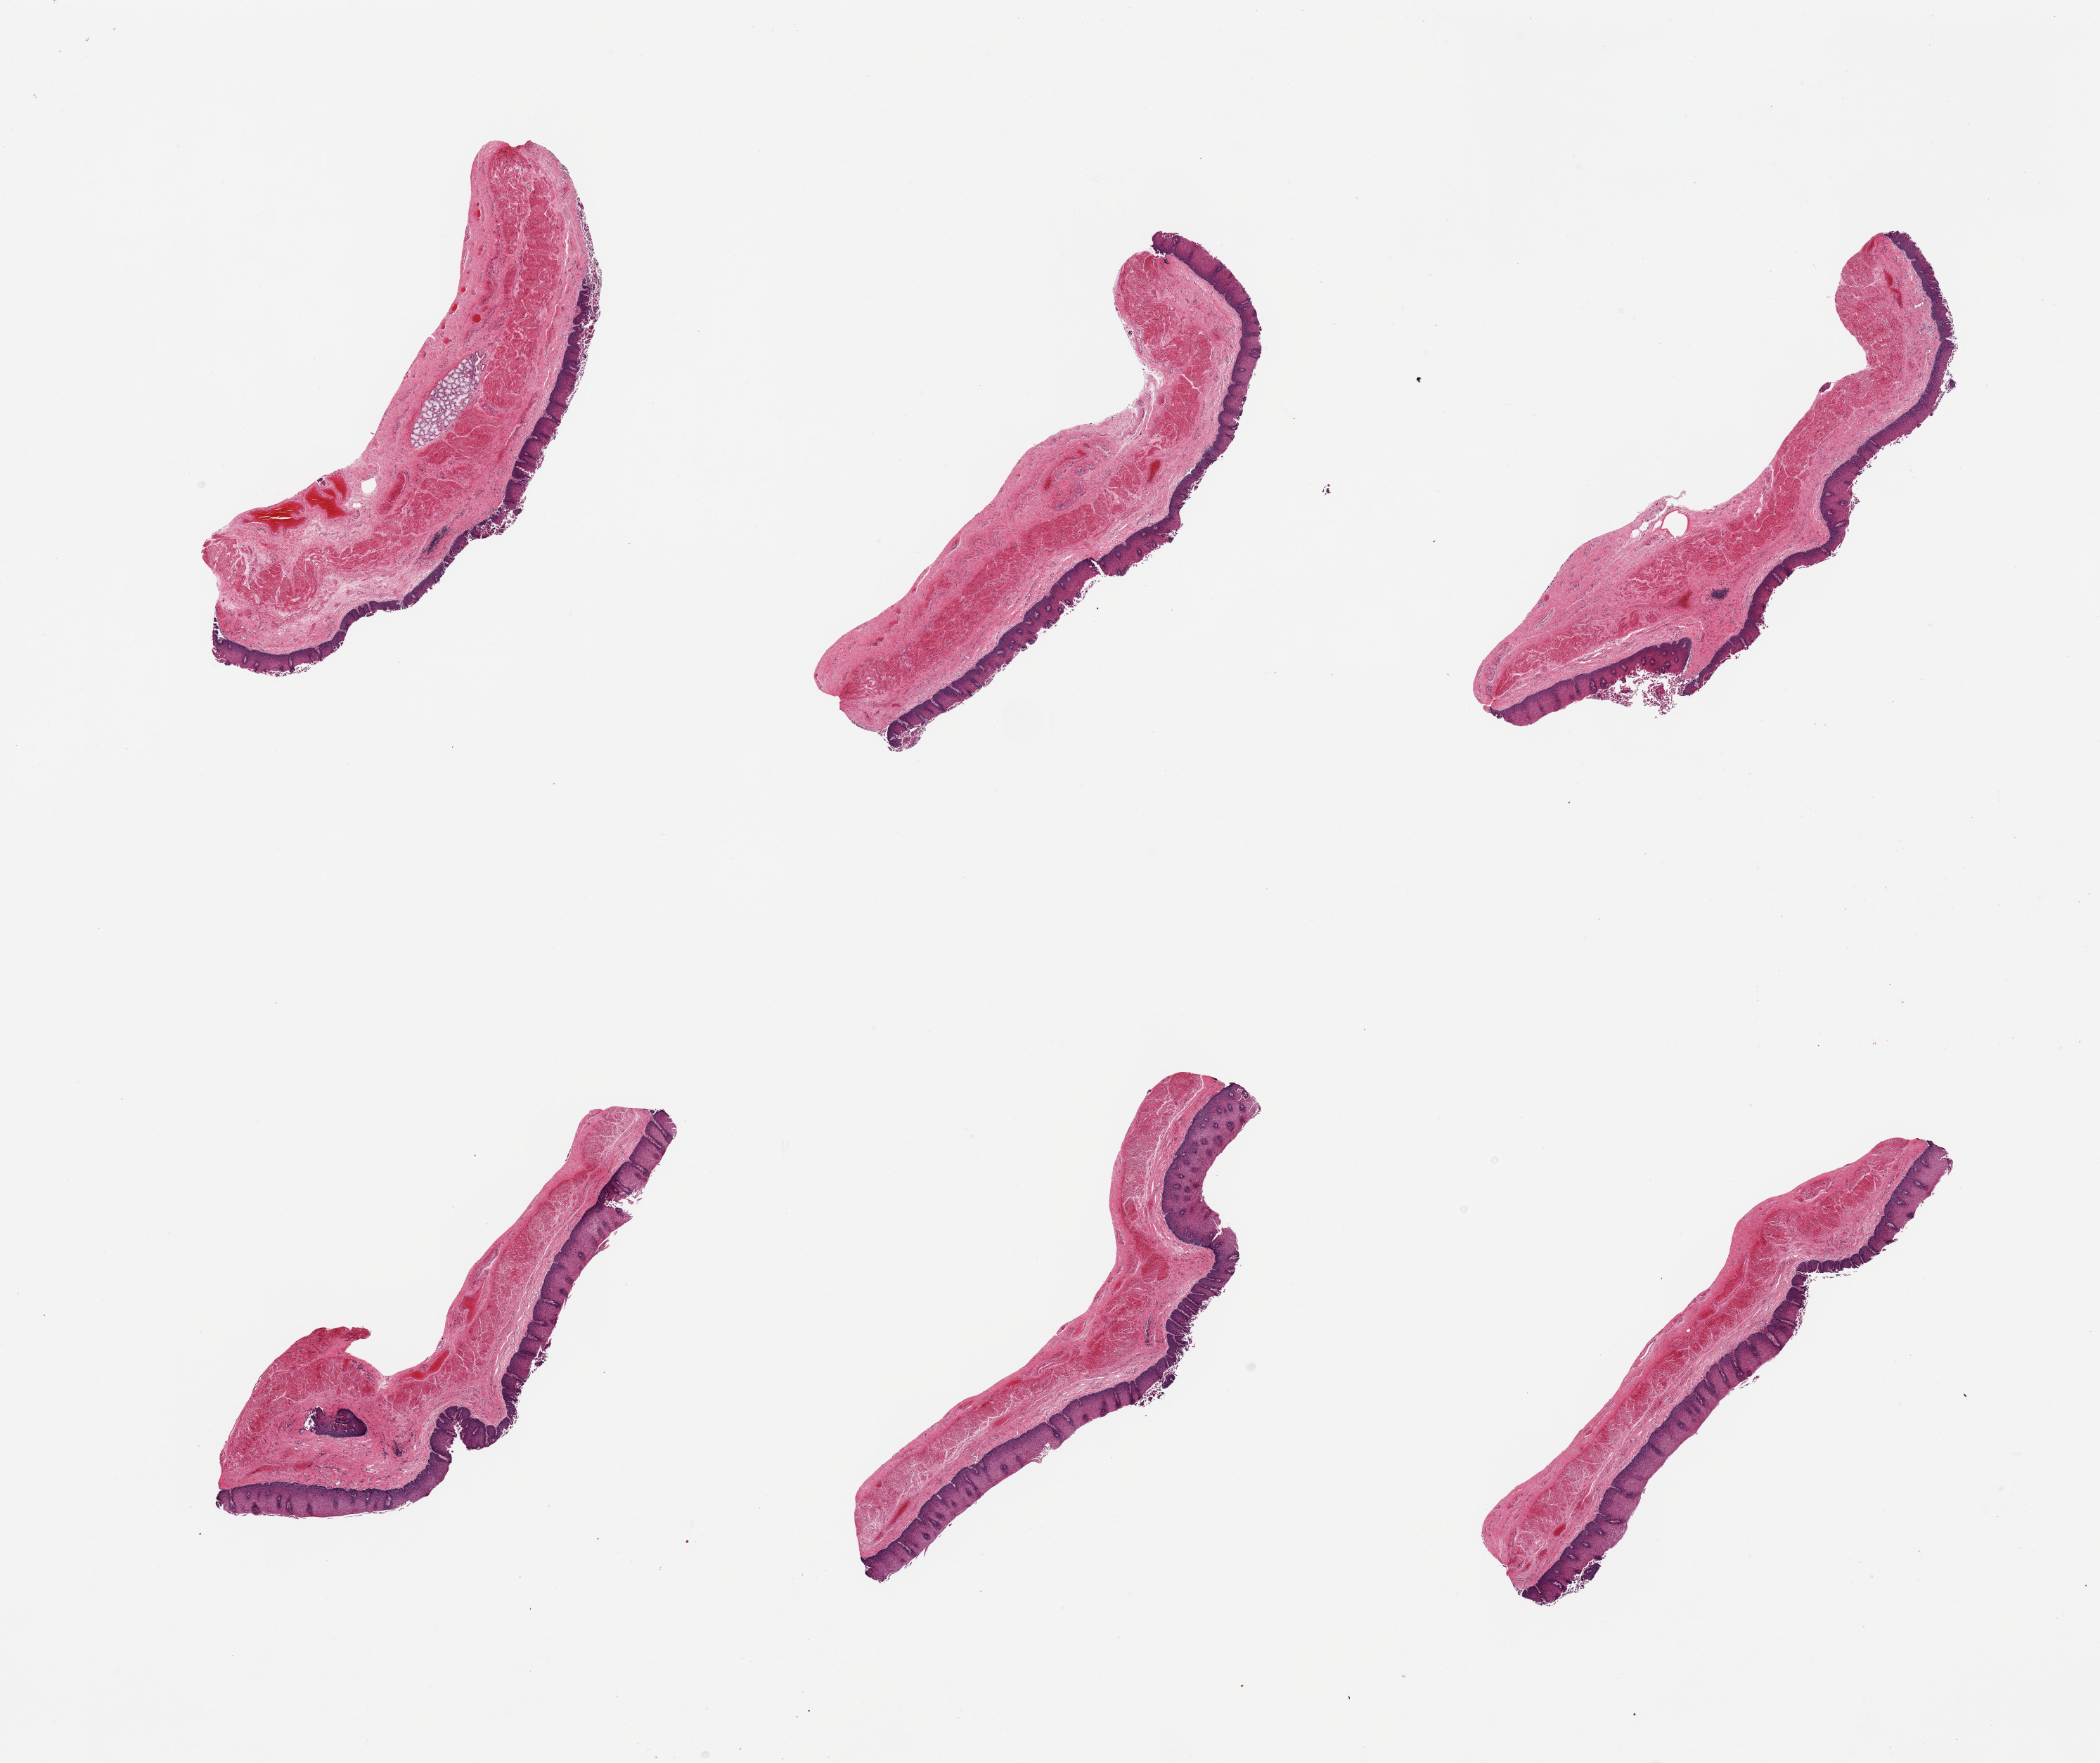
Digitized H&E-stained section, brightfield, low-resolution overview of the scanned area, about 23.6 x 19.8 mm (from a 20x scan), PAXgene-fixed, paraffin-embedded tissue, target tissue: esophageal mucous membrane, donor tissue sample. Donor sex: male.
Reviewer comment on this tissue sample: 6 pieces, squamous mucosa upt to ~0.25mm, approaching autolysis score in foci, rare mucus glands present.